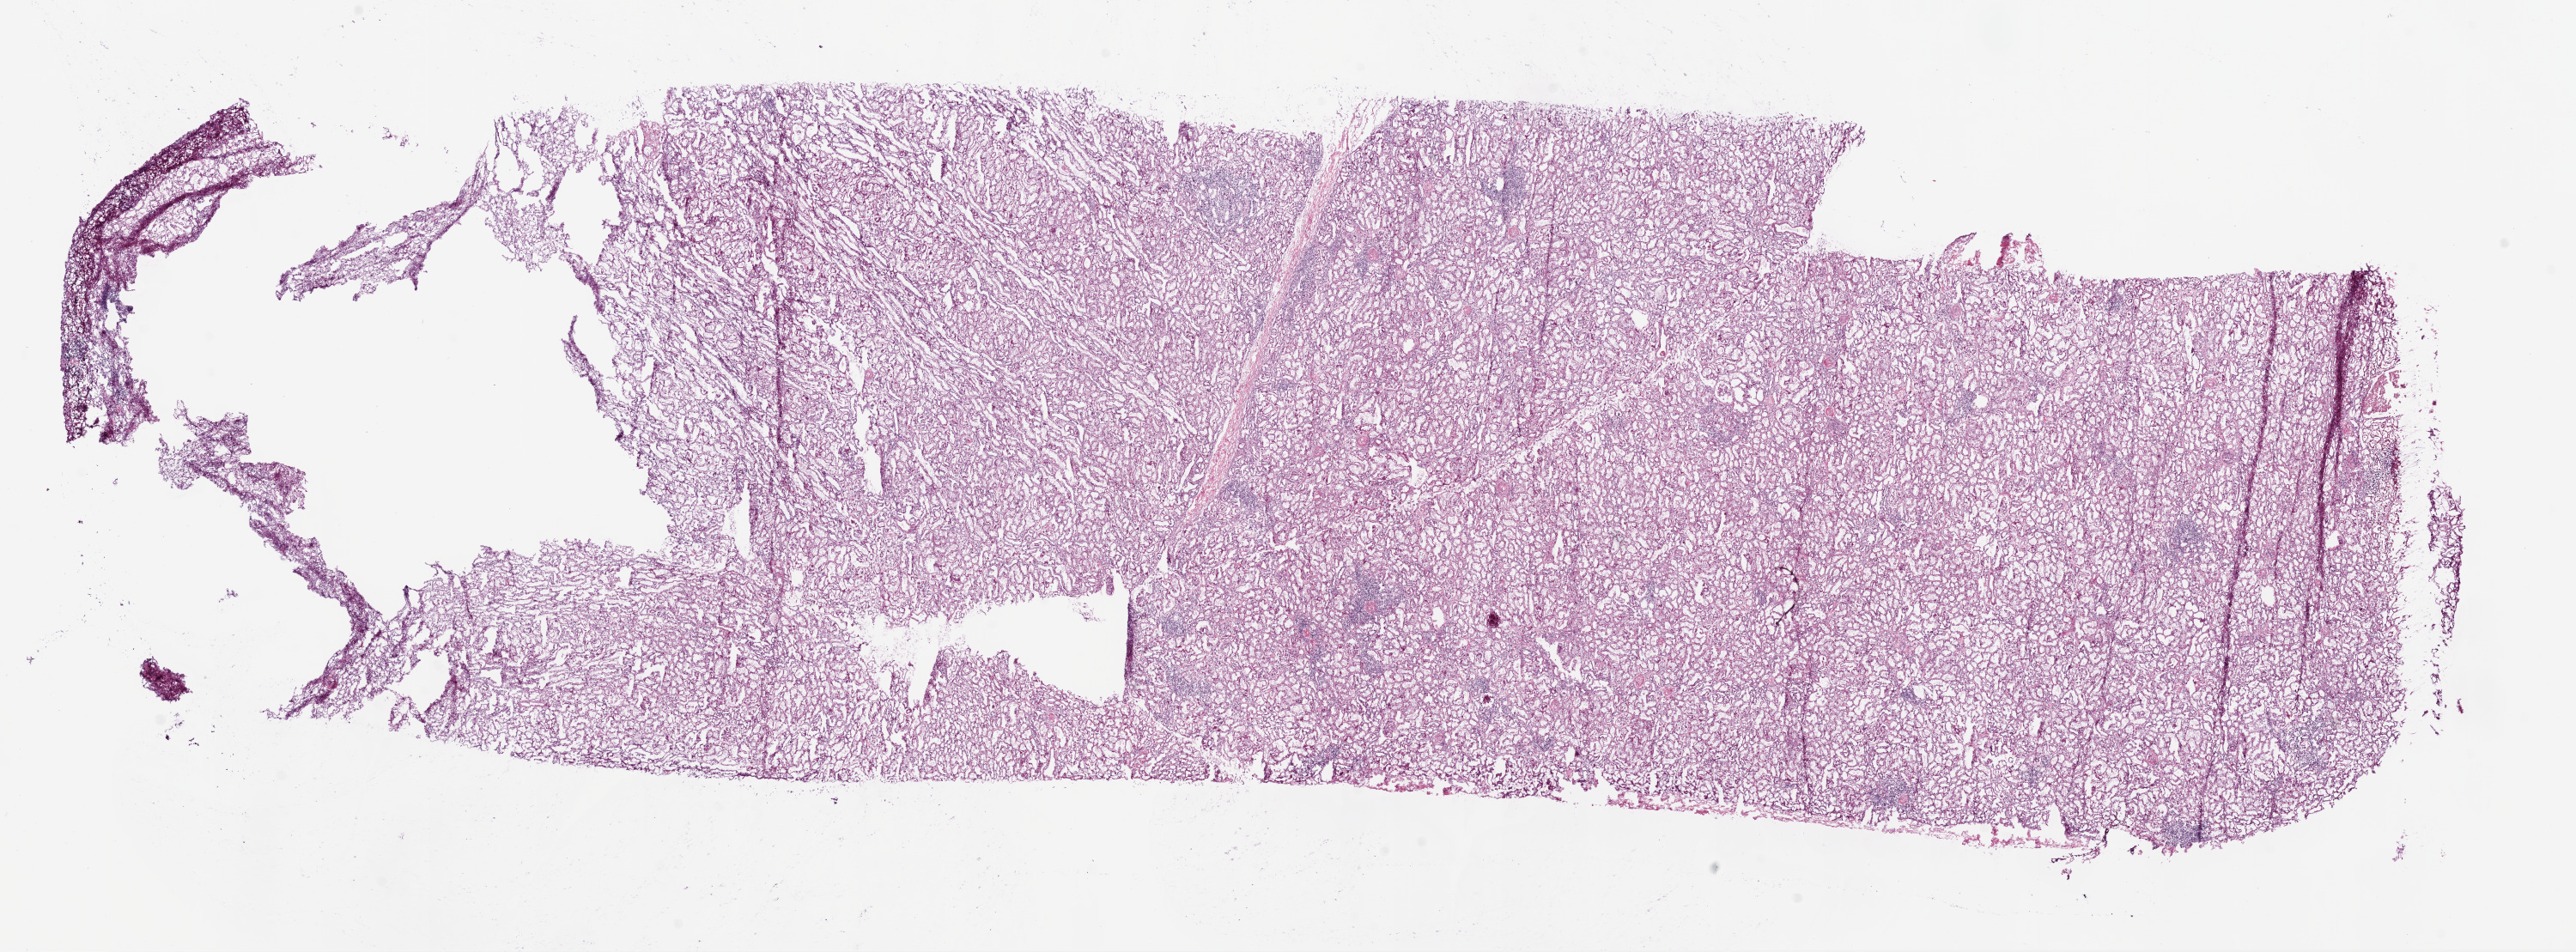
Whole-slide histology image, H&E-stained — low-resolution overview of the scanned area, about 24.1 x 8.9 mm (from a 20x scan). Frozen section from the bottom of the tissue portion. Kidney, solid tissue normal (non-tumour tissue) sample. Patient: female, age at initial diagnosis 67 years.
• this section: solid tissue normal (non-tumour) sample from the same patient
• patient diagnosis: Clear cell adenocarcinoma, NOS